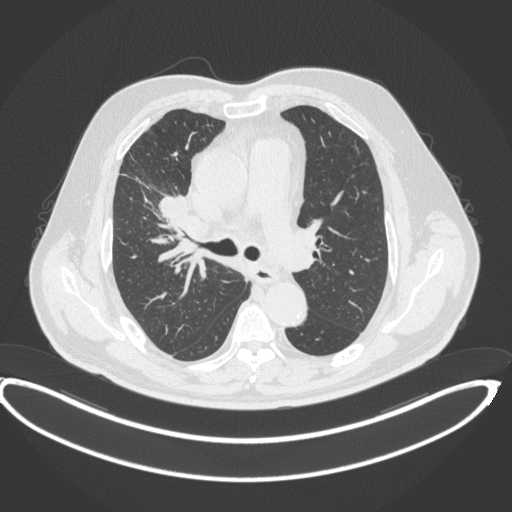
Chest CT, one axial slice; position 261 of 395 along the scan axis; reconstruction kernel B31f; 120 kVp; lung window (W 1500 / L -600 HU); 512 × 512 image matrix, field of view 448 × 448 mm. Male patient, age 62 years. Case-level facts recorded for this patient, not image findings: clinical TNM (as recorded): T1c N3 M1c.
Annotated regions visible in this slice (bounding box drawn by a radiologist):
- lung tumour (recorded histology: adenocarcinoma): bounding box [x1, y1, x2, y2] px = [157, 190, 191, 221]